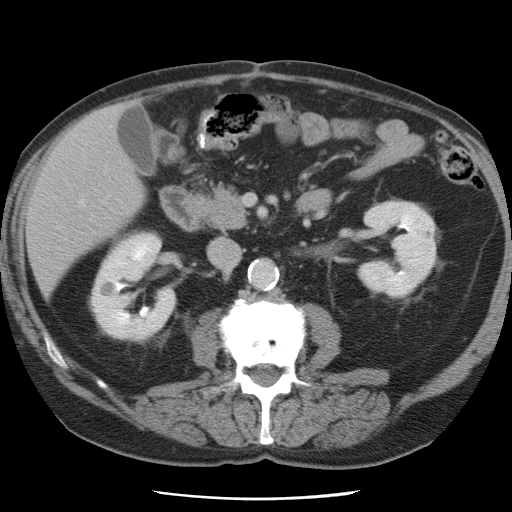
Contrast-enhanced abdominal CT, one axial slice; slice 28 of 78 in the series (ordered by position); 120 kVp; intravenous contrast given; soft-tissue window (W 400 / L 40 HU); 512 × 512 image matrix. Male patient, age 75 years. Case-level facts recorded for this patient, not image findings: diagnosis: colorectal cancer liver metastases, imaged before liver resection; multiple liver metastases: yes; largest metastasis: 2.4 cm; disease in both lobes: yes.
Structures marked on this image (expert manual segmentation):
- liver: box from (x=28, y=106) to (x=145, y=293) px
- planned liver remnant (the part of the liver to remain after resection): (x=29, y=117)–(x=145, y=294)